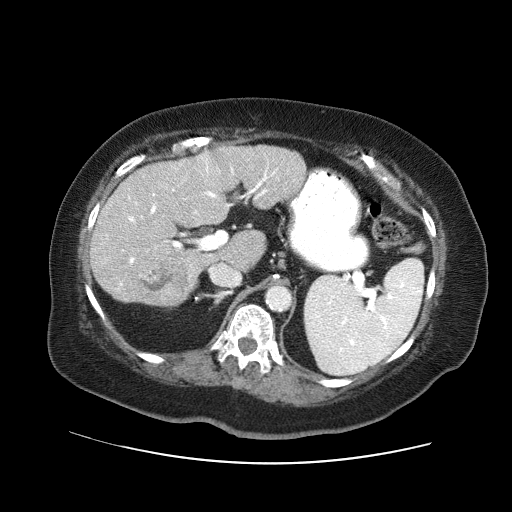
Contrast-enhanced abdominal CT (liver protocol), one axial slice. Slice 29 of 71 in the series (ordered by position). Reconstruction kernel STANDARD. 120 kVp. Soft-tissue window (W 400 / L 40 HU). 512 × 512 image matrix. Case-level facts recorded for this patient, not image findings: diagnosis: hepatocellular carcinoma (patient treated with transarterial chemoembolisation; whether this scan precedes or follows treatment is not stated here); TNM stage (as recorded): Stage-II; Child-Pugh class: A; tumour differentiation: poorly differentiated; tumour nodularity: multinodular.
Annotated regions visible in this slice (semi-automatic segmentation, software-assisted and operator-edited):
- liver parenchyma outside the tumour (the mass and vessels are separate outlines, so this box may not span the whole liver): box from (x=90, y=144) to (x=306, y=306) px
- mass: (x=134, y=246)–(x=188, y=298)
- liver vessels: (x=119, y=159)–(x=276, y=286)